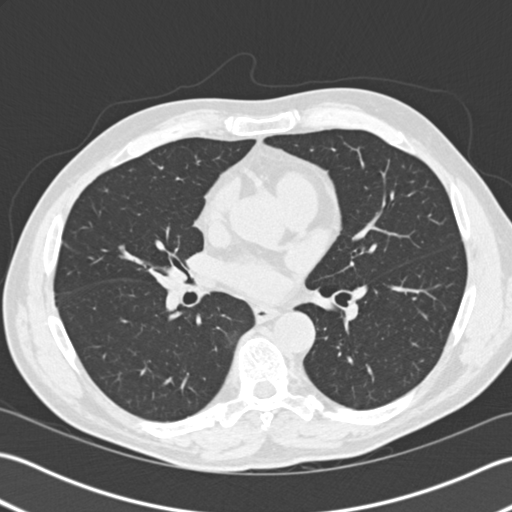
Low-dose screening chest CT, axial slice. Second annual screen. Lung window (W 1500 / L -600 HU). Standard (soft-tissue) reconstruction kernel (B30f). 512 × 512 image matrix, field of view 350 × 350 mm. Male participant, aged 57 years at enrolment. Former smoker at enrolment.
Expert reader's lesion annotation, bounding box <156,253,196,290> (left, top, right, bottom; pixels). Screening reader's record for this exam: no non-calcified nodule ≥4 mm recorded. Official screen result: negative screen, significant abnormalities not suspicious for lung cancer.